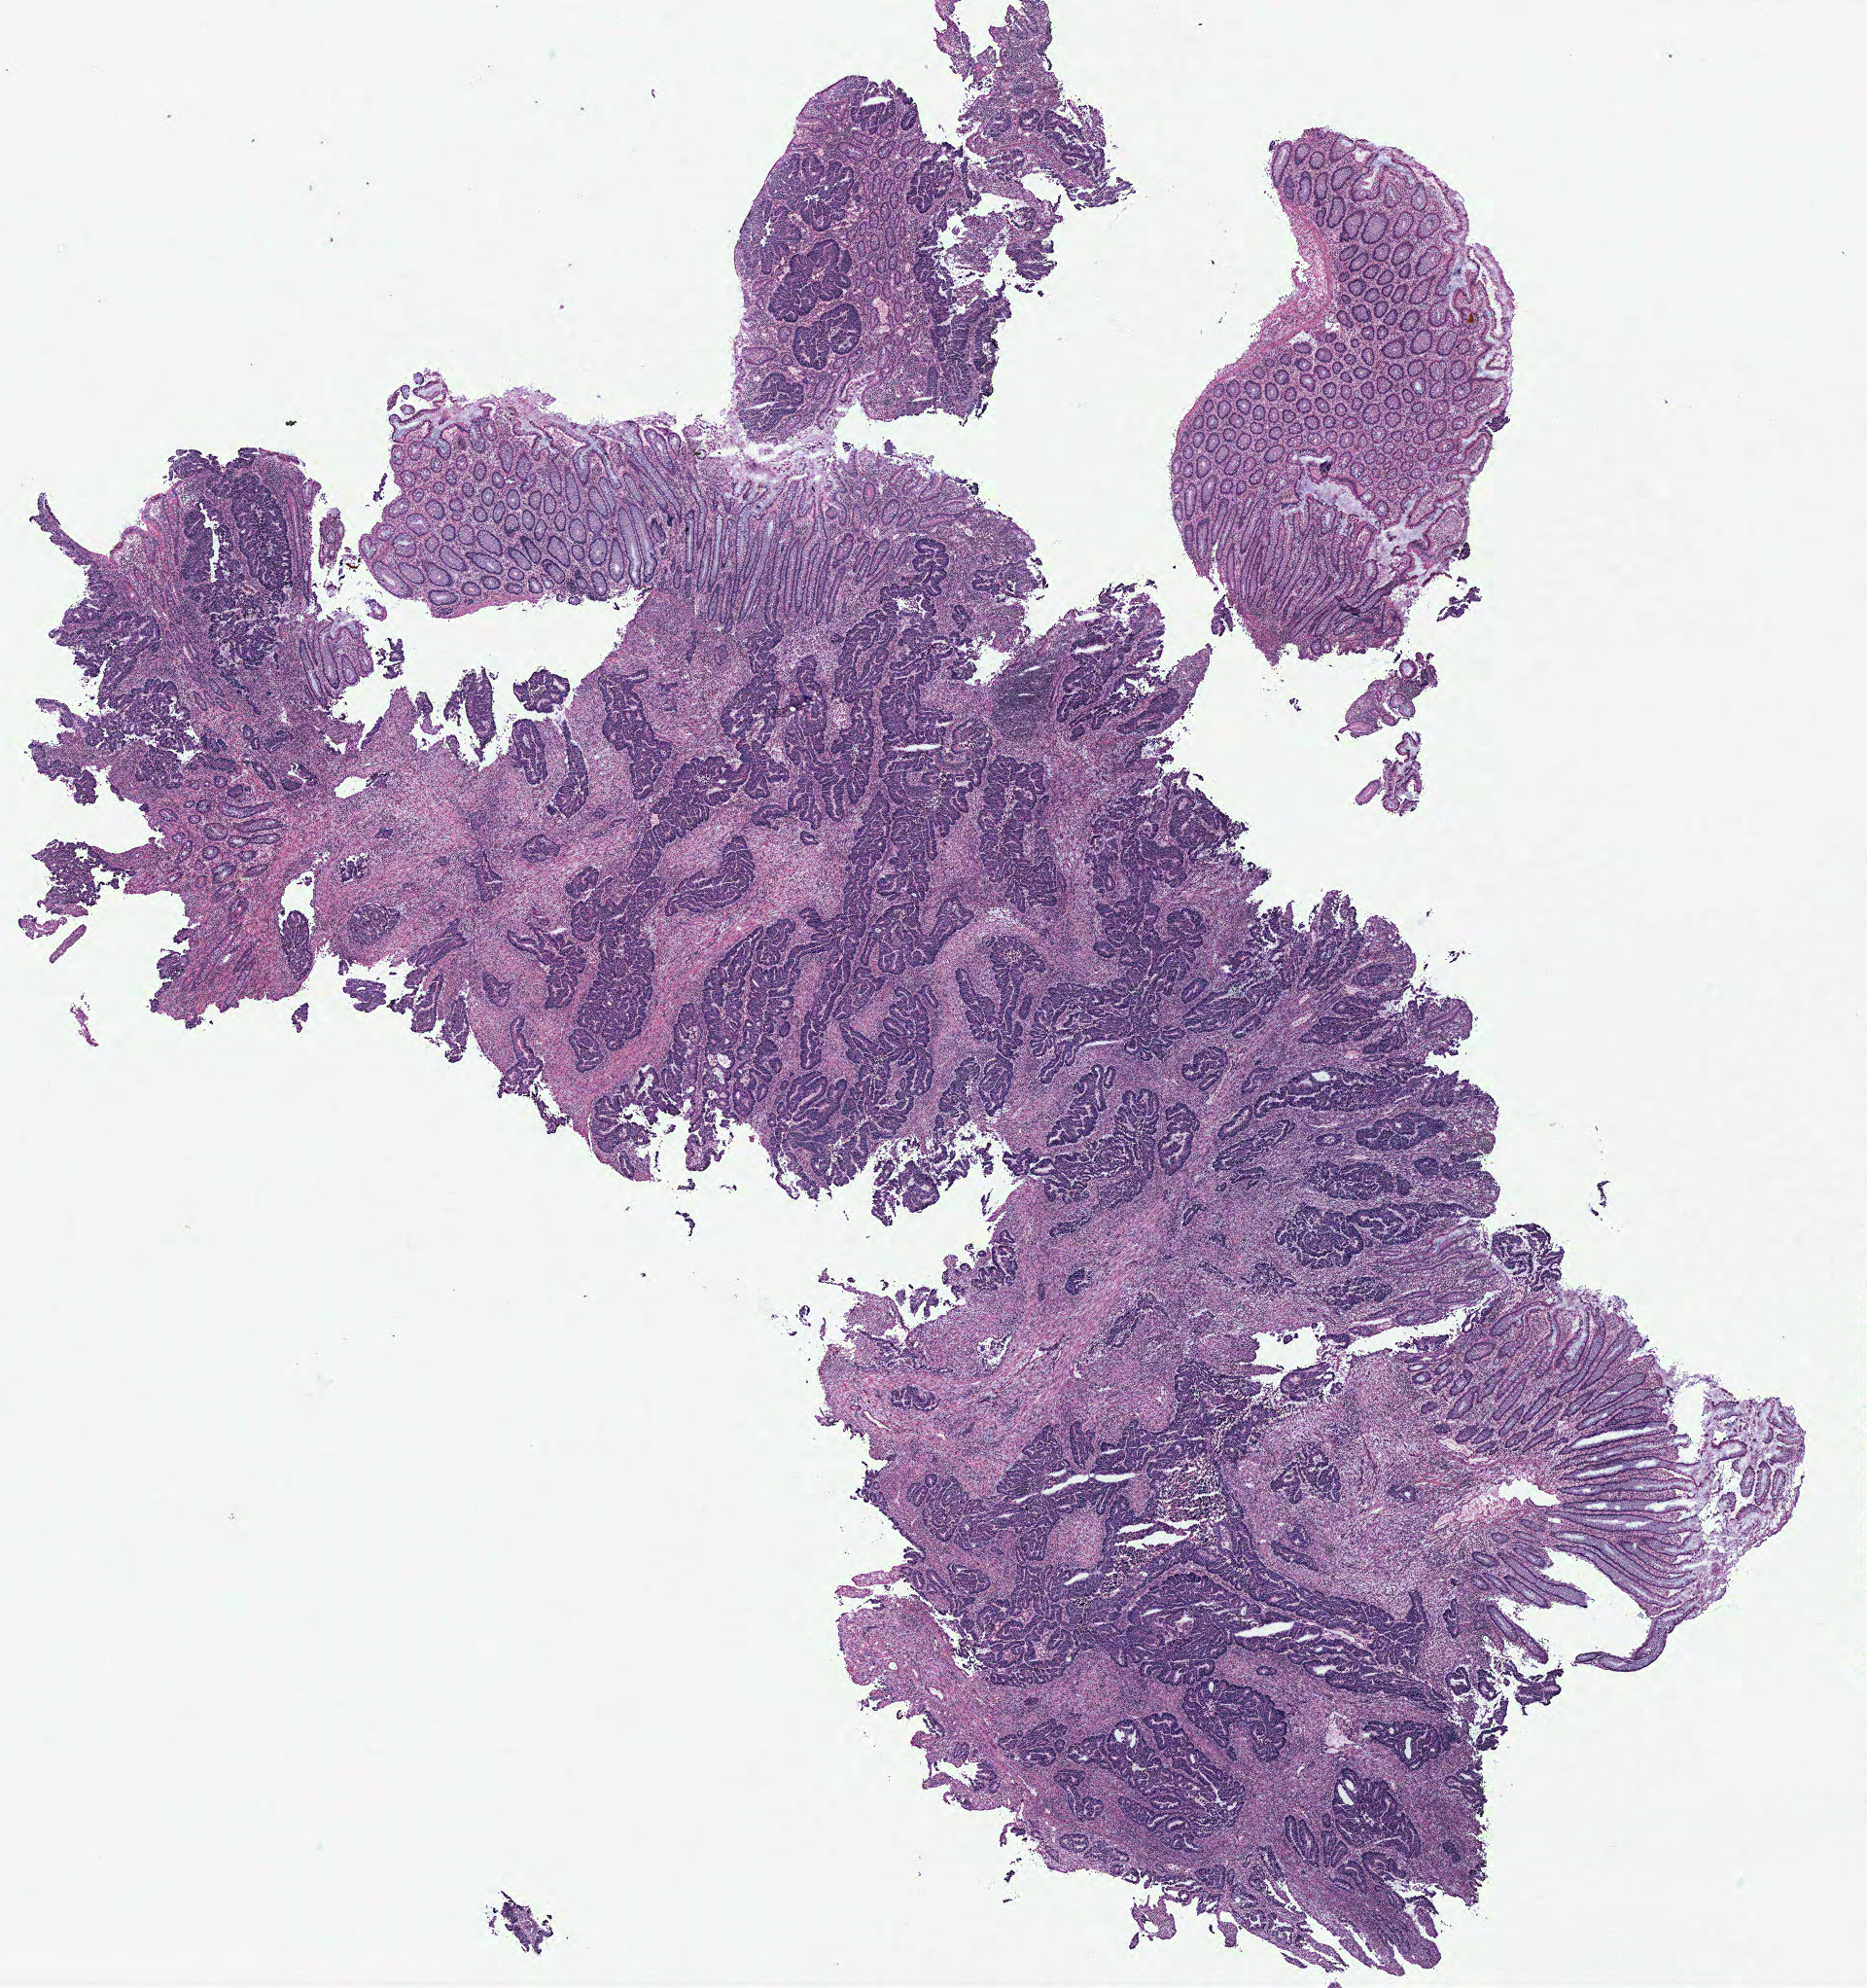
Hematoxylin and eosin (H&E) stained whole-slide image — low-resolution overview of the scanned area, about 15.4 x 16.4 mm (from a 40x scan), colon, normal (non-tumour) tissue. Patient: female, age 53 years.
• this section: normal (non-tumour) tissue from the same patient
• patient diagnosis: Adenocarcinoma, NOS